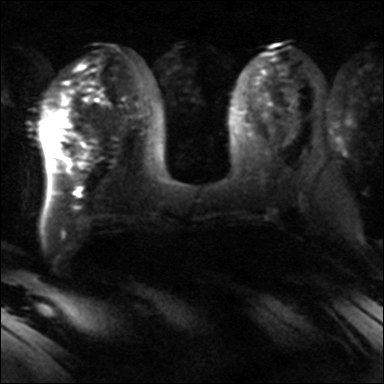
Breast MRI, one axial slice. Position 17 of 40 along the scan axis. Diffusion-weighted series; image 2 of 4 stored at this slice position (different b-values; order by instance number). 3 T. 384 × 384 image matrix, field of view 320 × 320 mm. Female patient.
Annotated regions visible in this slice (manually delineated by an expert):
- tumour on diffusion-weighted imaging: bounding box <50,137,57,143> (left, top, right, bottom; pixels)